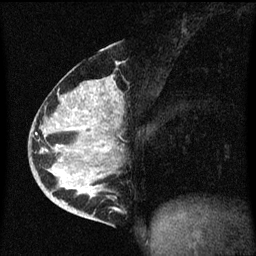
Breast MRI (dynamic contrast-enhanced), one sagittal slice. Position 28 of 60 along the scan axis. Dynamic contrast-enhanced series, image 2 of 3 at this slice position (ordered by acquisition). 1.5 T. TE 4.2 ms, TR 8.4 ms. 256 × 256 image matrix, field of view 200 × 200 mm. Female patient, age 34 years. Case-level facts recorded for this patient, not image findings: setting: breast cancer imaged before/during neoadjuvant chemotherapy; receptor status: HR-positive, HER2-negative.
Structures marked on this image (semi-automatically segmented with operator editing):
- analysis volume of interest (the breast-tissue region the enhancement analysis was run in; not a lesion): bounding box <34,48,123,215> (left, top, right, bottom; pixels)
- tumour enhancement mask (voxels above the 70 % enhancement threshold inside the analysis volume of interest): <54,84,111,195>